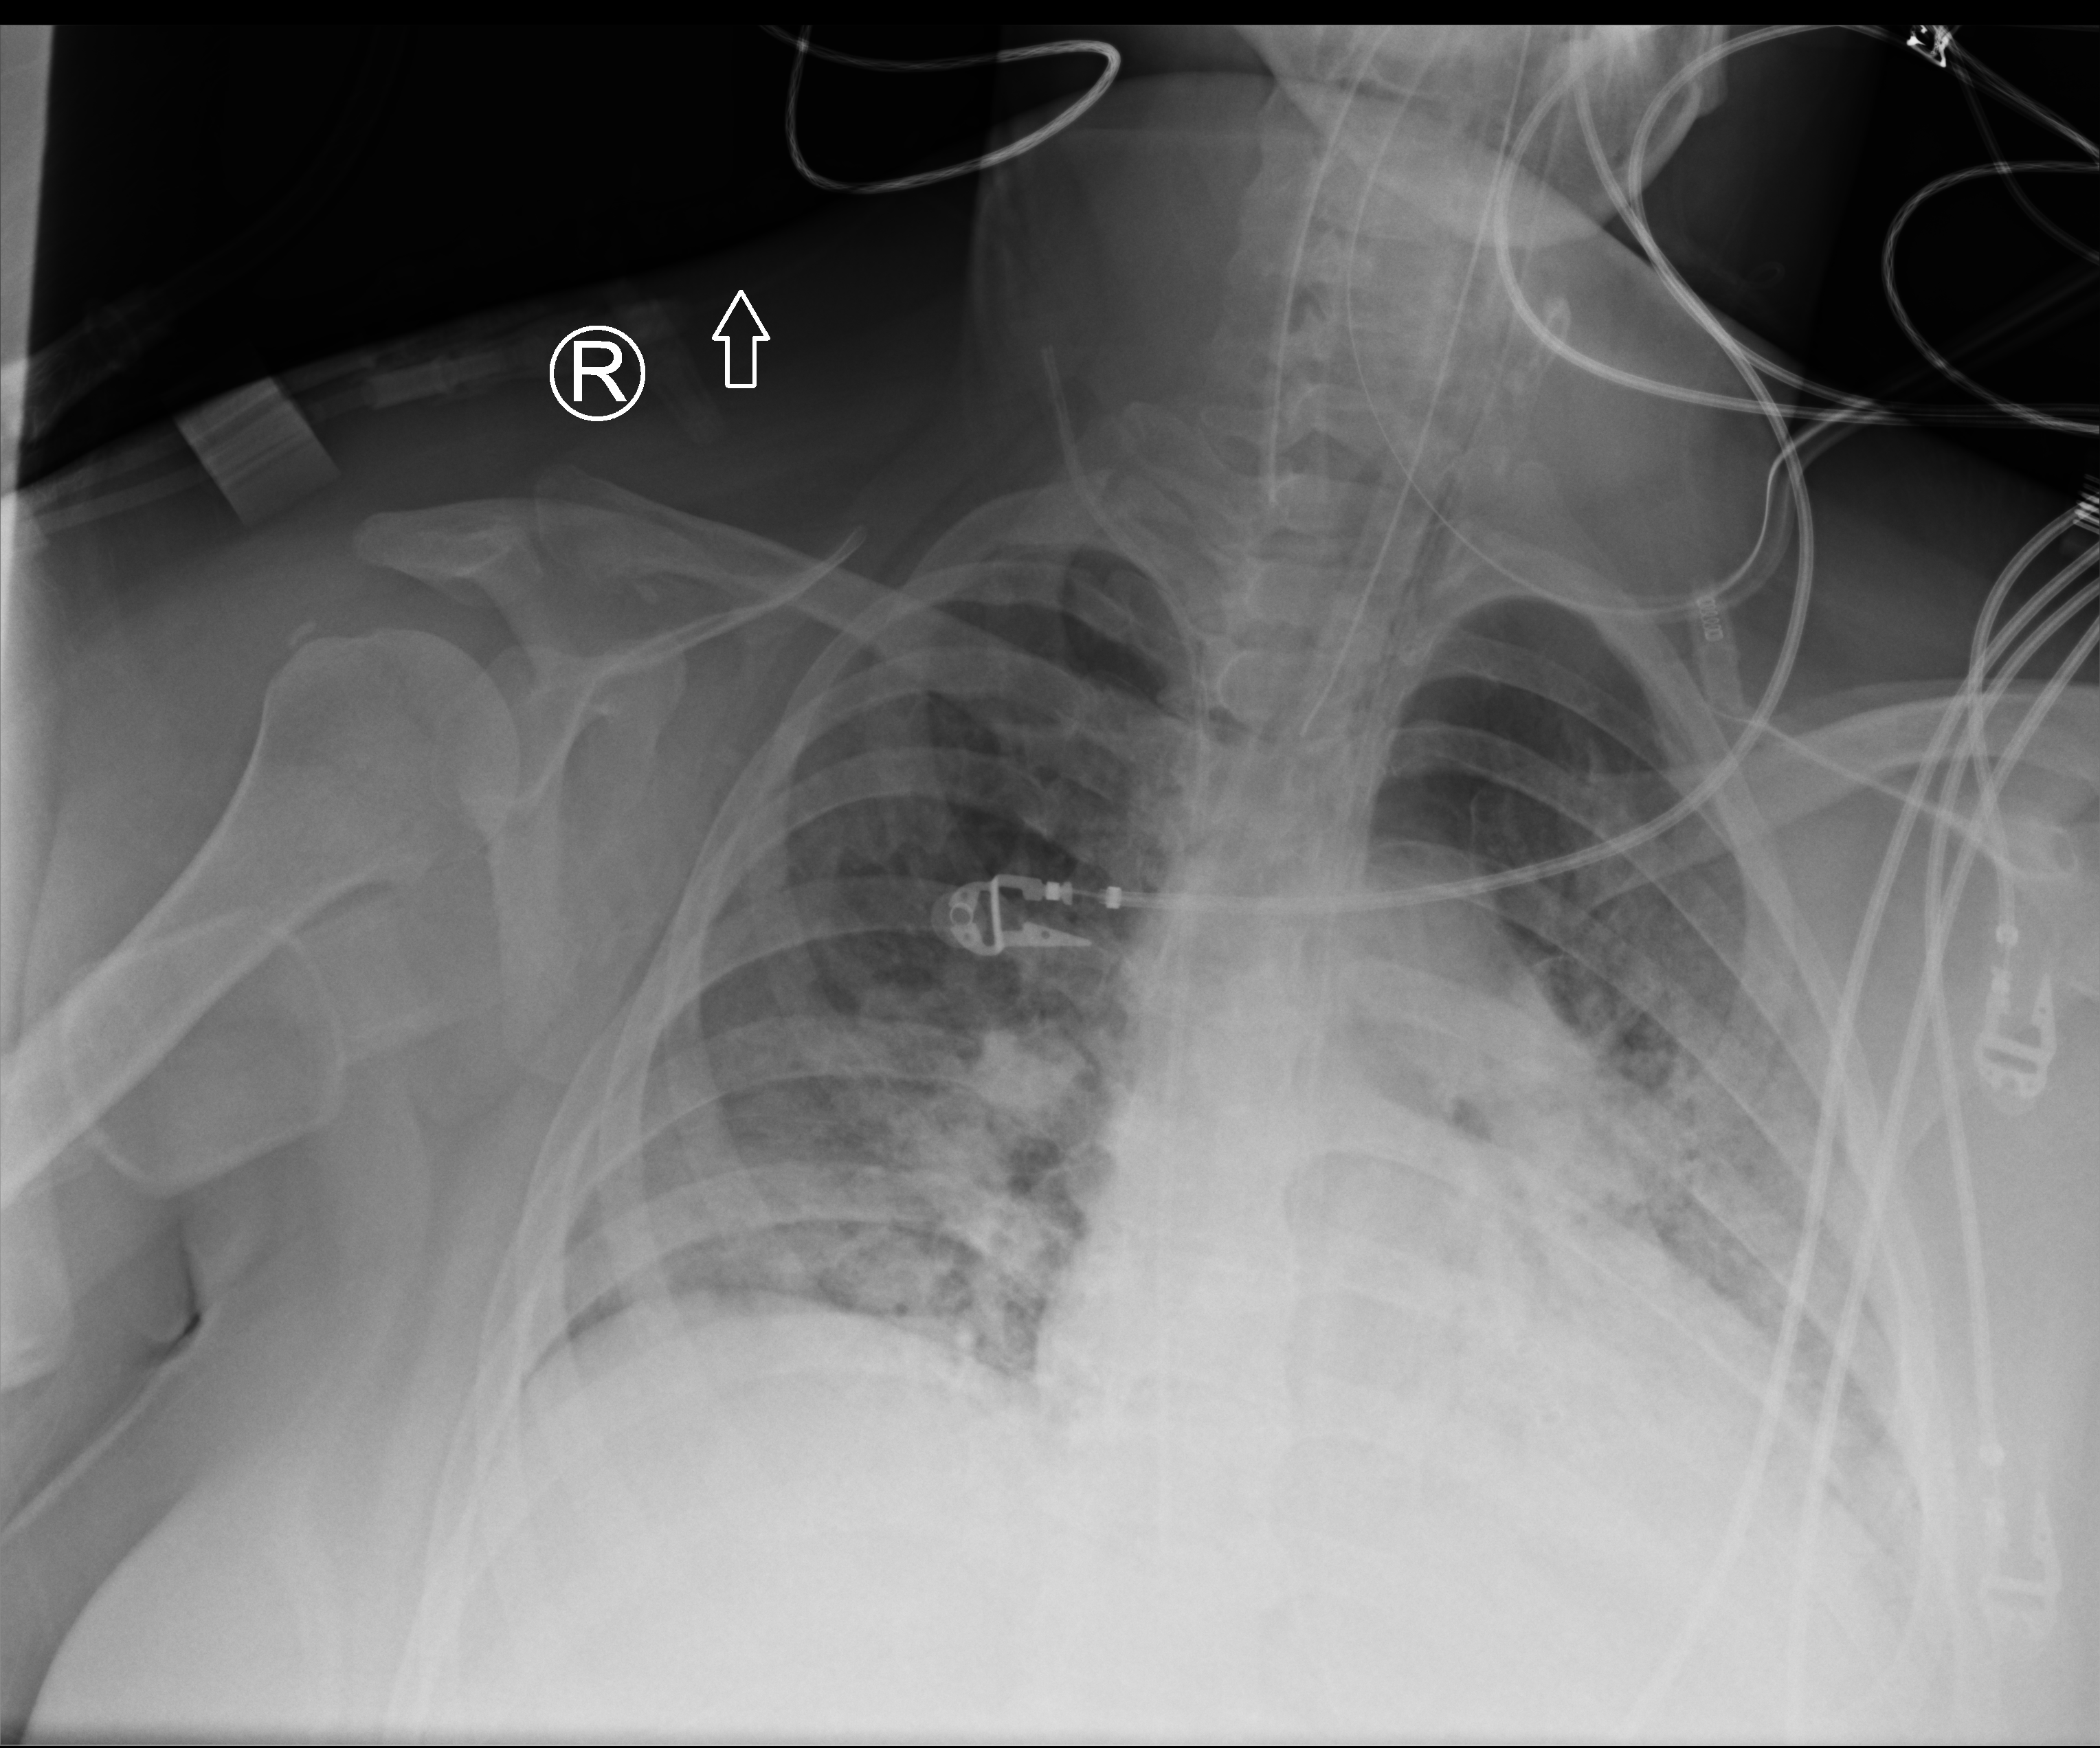
Bedside chest radiograph (computed radiography); anteroposterior (AP) projection. Female patient hospitalised with COVID-19, age 18–59 years.
Hospital-stay facts (about this admission, not read from this image; timing relative to this image not recorded): mechanically ventilated during this hospital stay: yes.